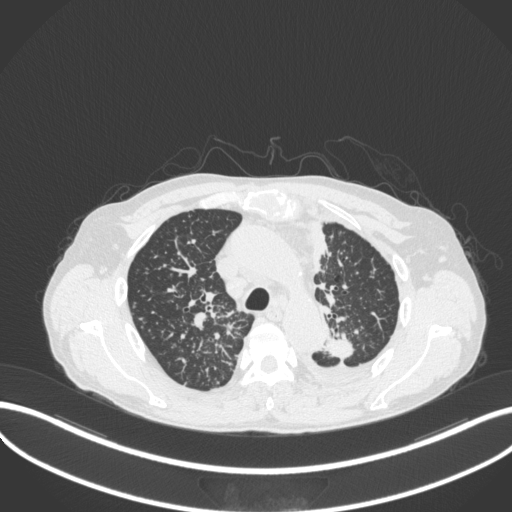
Chest CT, one axial slice; position 258 of 319 along the scan axis; reconstruction kernel B31f; 120 kVp; lung window (W 1500 / L -600 HU); 512 × 512 image matrix, field of view 400 × 400 mm. Patient: male, 58 years. Case-level facts recorded for this patient, not image findings: clinical TNM (as recorded): T1c N3 M1.
Outlined on this slice (bounding box drawn by a radiologist):
- lung tumour (recorded histology: adenocarcinoma): bounding box (x1, y1, x2, y2) in pixels: (323, 333, 363, 362)